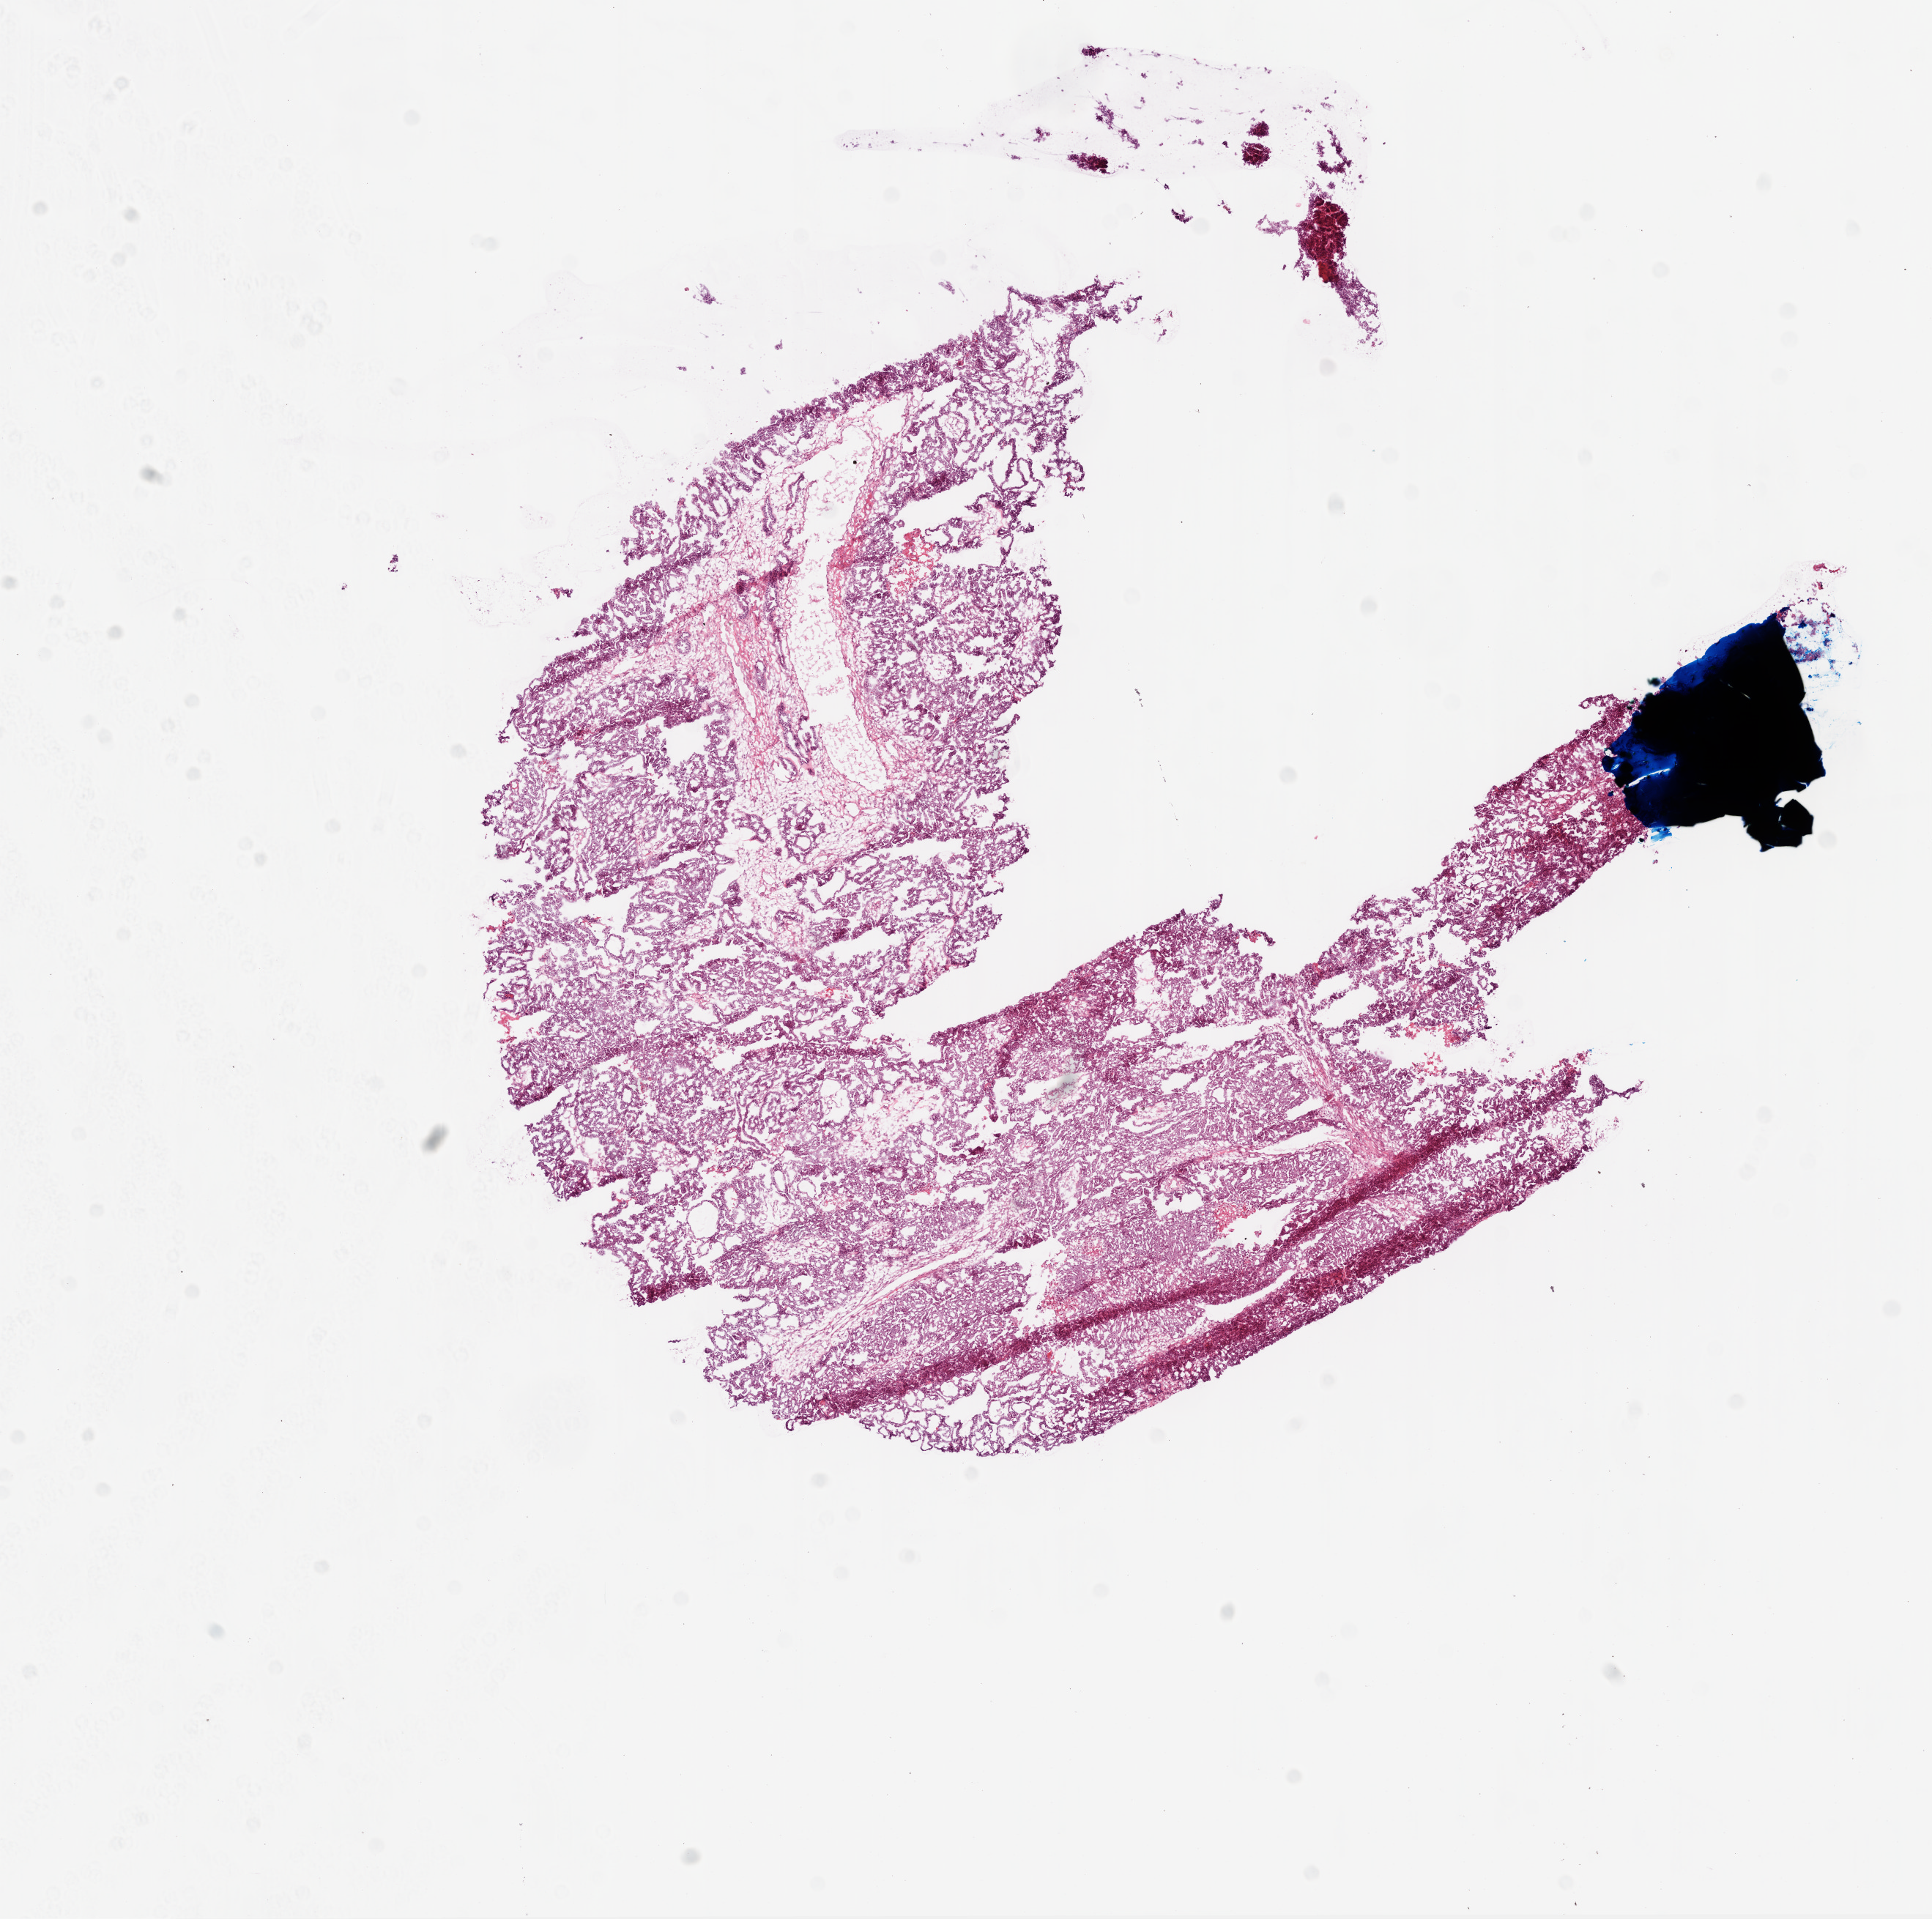
Whole-slide histology image, H&E — a low-resolution overview of the entire scanned area, about 10.6 x 10.6 mm (acquisition: 20x scan), frozen section from the top of the tissue portion, primary tumour sample from the ovary. Female patient; age at initial diagnosis 67 years. Histologic grade: G3 (poorly differentiated). Composition of this section per pathologist review: tumour cells 90%, tumour nuclei 90%, normal cells 5%, stromal cells 5%, necrosis 0%.
FIGO stage: IIIC. Pathologic diagnosis: Serous cystadenocarcinoma, NOS. Laterality: left.